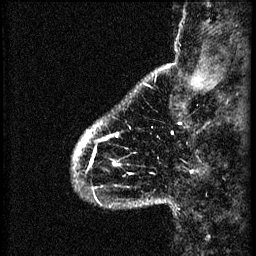
Breast MRI (dynamic contrast-enhanced), one sagittal slice; position 7 of 60 along the scan axis; 3 images stored at this slice position (order not interpretable as contrast timing); 1.5 T; TE 4.2 ms, TR 8.2 ms; 2.2 mm slice thickness; 256 × 256 image matrix, field of view 180 × 180 mm. Female patient, age 41 years.
Outlined on this slice (semi-automatic segmentation, software-assisted and operator-edited):
- analysis volume of interest (the breast-tissue region the enhancement analysis was run in; not a lesion): bounding box <75,126,157,207> (left, top, right, bottom; pixels)
- tumour enhancement mask (voxels above the 70 % enhancement threshold inside the analysis volume of interest): <76,134,132,189>